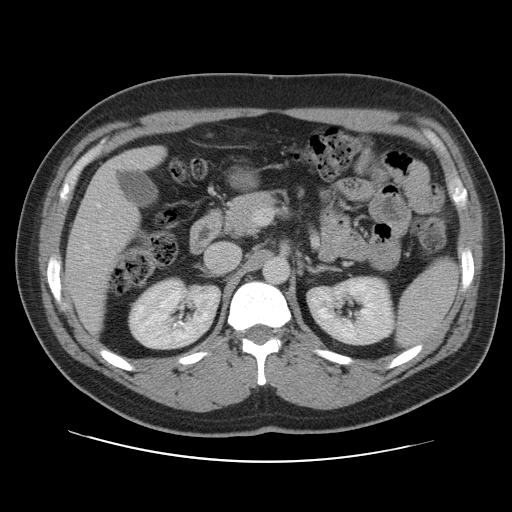
Contrast-enhanced abdominal CT, one axial slice; slice 59 of 109 in the series (ordered by position); soft-tissue window (W 400 / L 40 HU); 5 mm slice thickness; 512 × 512 image matrix, field of view 402 × 402 mm. Male patient, age 35 years. From the clinical record (not read from this slice): diagnosis: colorectal cancer liver metastases, imaged before liver resection; multiple liver metastases: yes; largest metastasis: 2.8 cm; chemotherapy before resection: yes.
Outlined on this slice (manually delineated by an expert):
- liver: bounding box <67,147,163,329> (left, top, right, bottom; pixels)
- planned liver remnant (the part of the liver to remain after resection): <67,147,163,330>